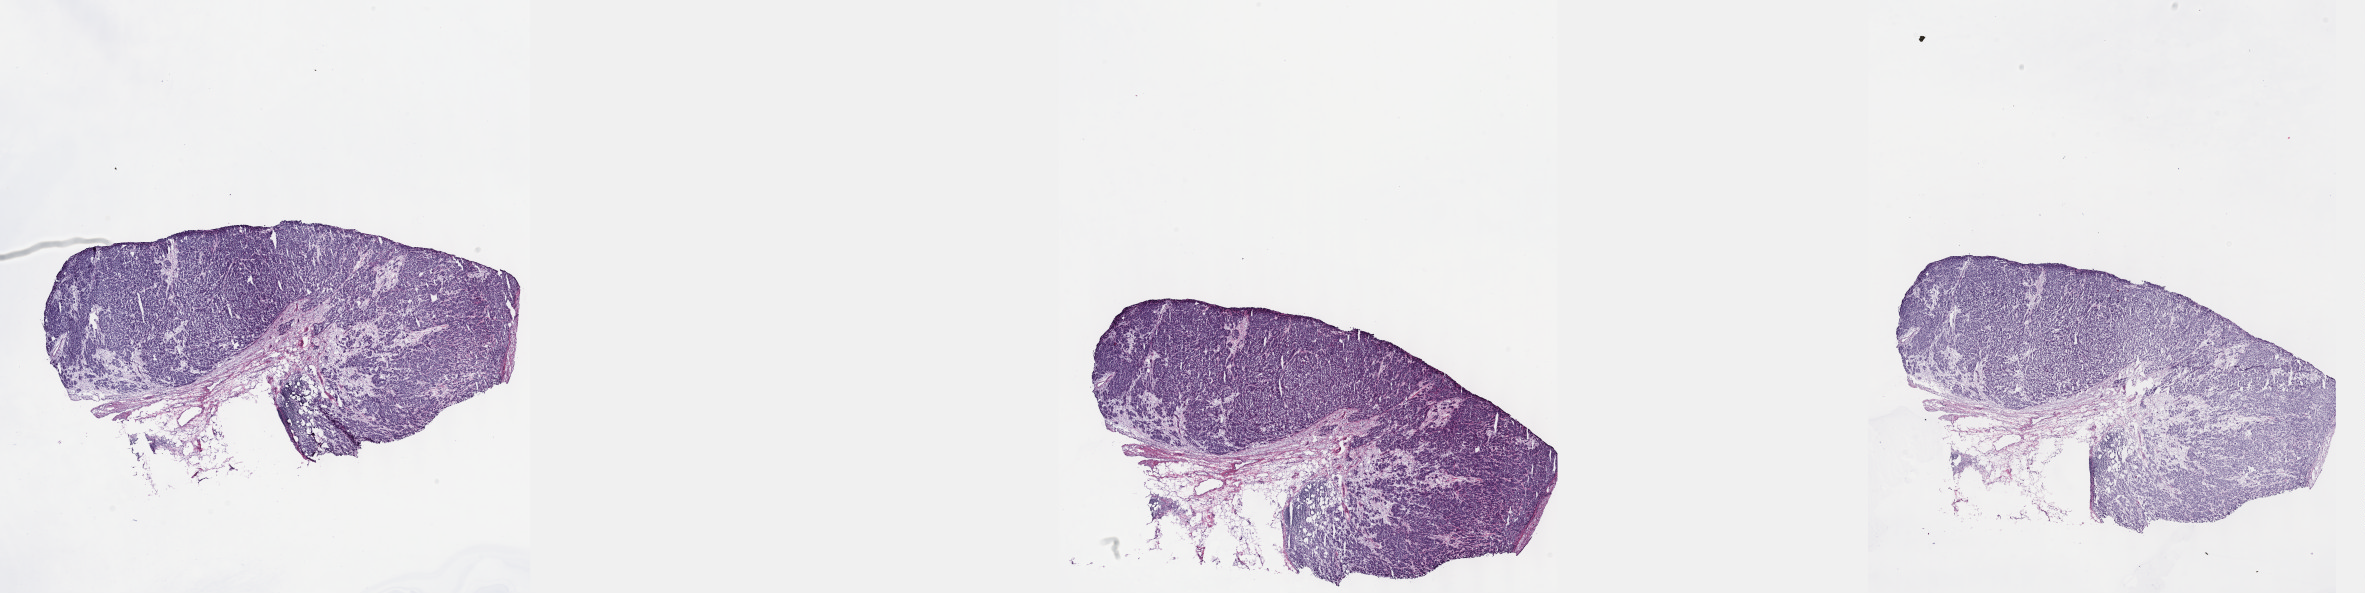
Whole-slide histology image, H&E, shown as a low-resolution overview of the whole scanned area (about 38.2 x 9.6 mm). Frozen section from the top of the tissue portion. Breast, primary tumour sample. Female, age 55 years at initial diagnosis. Composition of this section per pathologist review: tumour cells 70%, tumour nuclei 70%, normal cells 0%, stromal cells 30%, necrosis 0%. Infiltration values recorded for this section: lymphocyte infiltration 40%, monocyte infiltration 20%, neutrophil infiltration 20%.
- lymph nodes positive (case pathology): 4 of 13 examined
- histologic diagnosis: Lobular carcinoma, NOS
- laterality: left